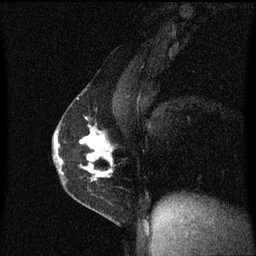
Breast MRI (dynamic contrast-enhanced), one sagittal slice; position 36 of 60 along the scan axis; dynamic contrast-enhanced series, image 2 of 3 at this slice position (ordered by acquisition); 1.5 T; TE 4.2 ms, TR 8.4 ms; 2 mm slice thickness; 256 × 256 image matrix, field of view 200 × 200 mm. Female patient, age 40 years.
Outlined on this slice (semi-automatically segmented with operator editing):
- analysis volume of interest (the breast-tissue region the enhancement analysis was run in; not a lesion): bounding box <57,110,115,191> (left, top, right, bottom; pixels)
- tumour enhancement mask (voxels above the 70 % enhancement threshold inside the analysis volume of interest): <57,126,113,181>